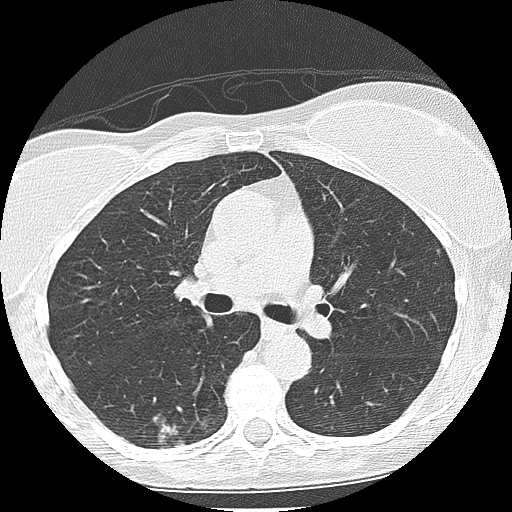
Low-dose screening chest CT, one axial slice; position 129 of 225 along the scan axis; reconstruction kernel LUNG; lung window (W 1500 / L -600 HU); 2.5 mm slice thickness; 512 × 512 image matrix, field of view 300 × 300 mm.
Structures marked on this image (outlined manually by an expert reader):
- lesion 1 (tumor, lower lobe of right lung): box from (x=158, y=422) to (x=186, y=450) px